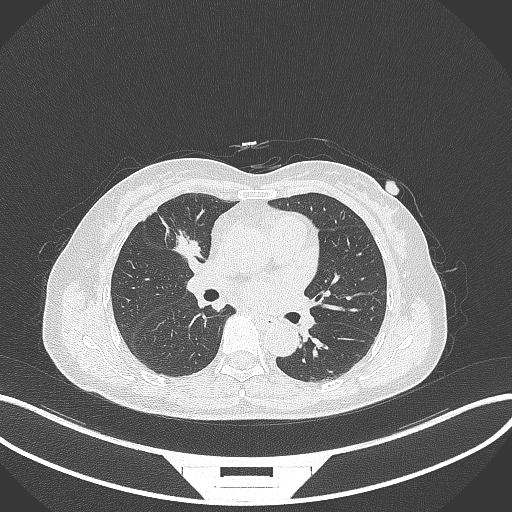
Chest CT, one axial slice; position 161 of 284 along the scan axis; reconstruction kernel B70f; lung window (W 1500 / L -600 HU); 1 mm slice thickness; 512 × 512 image matrix, field of view 400 × 400 mm. Female patient, age 51 years. Case-level facts recorded for this patient, not image findings: clinical TNM (as recorded): T1c N0 M0; histopathological grade: G2.
Annotated regions visible in this slice (bounding box drawn by a radiologist):
- lung tumour (recorded histology: adenocarcinoma): bounding box (x1, y1, x2, y2) in pixels: (168, 224, 206, 261)